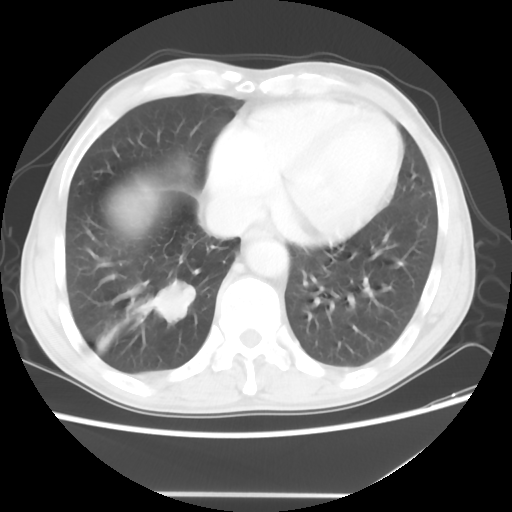
Chest CT, one axial slice; slice 15 of 56 in the series (ordered by position); 120 kVp; lung window (W 1500 / L -600 HU); 512 × 512 image matrix, field of view 344 × 344 mm. Patient: male, 65 years. From the clinical record (not read from this slice): clinical TNM (as recorded): T1c N3 M0.
Outlined on this slice (bounding box drawn by a radiologist):
- lung tumour (recorded histology: small cell carcinoma): bounding box (x1, y1, x2, y2) in pixels: (140, 277, 198, 326)